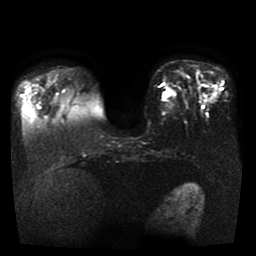
Breast MRI, one axial slice. Position 12 of 41 along the scan axis. Diffusion-weighted series; image 2 of 4 stored at this slice position (different b-values; order by instance number). 1.5 T. 256 × 256 image matrix, field of view 330 × 330 mm. Female patient.
Structures marked on this image (manually delineated by an expert):
- tumour on diffusion-weighted imaging: box from (x=162, y=90) to (x=172, y=101) px